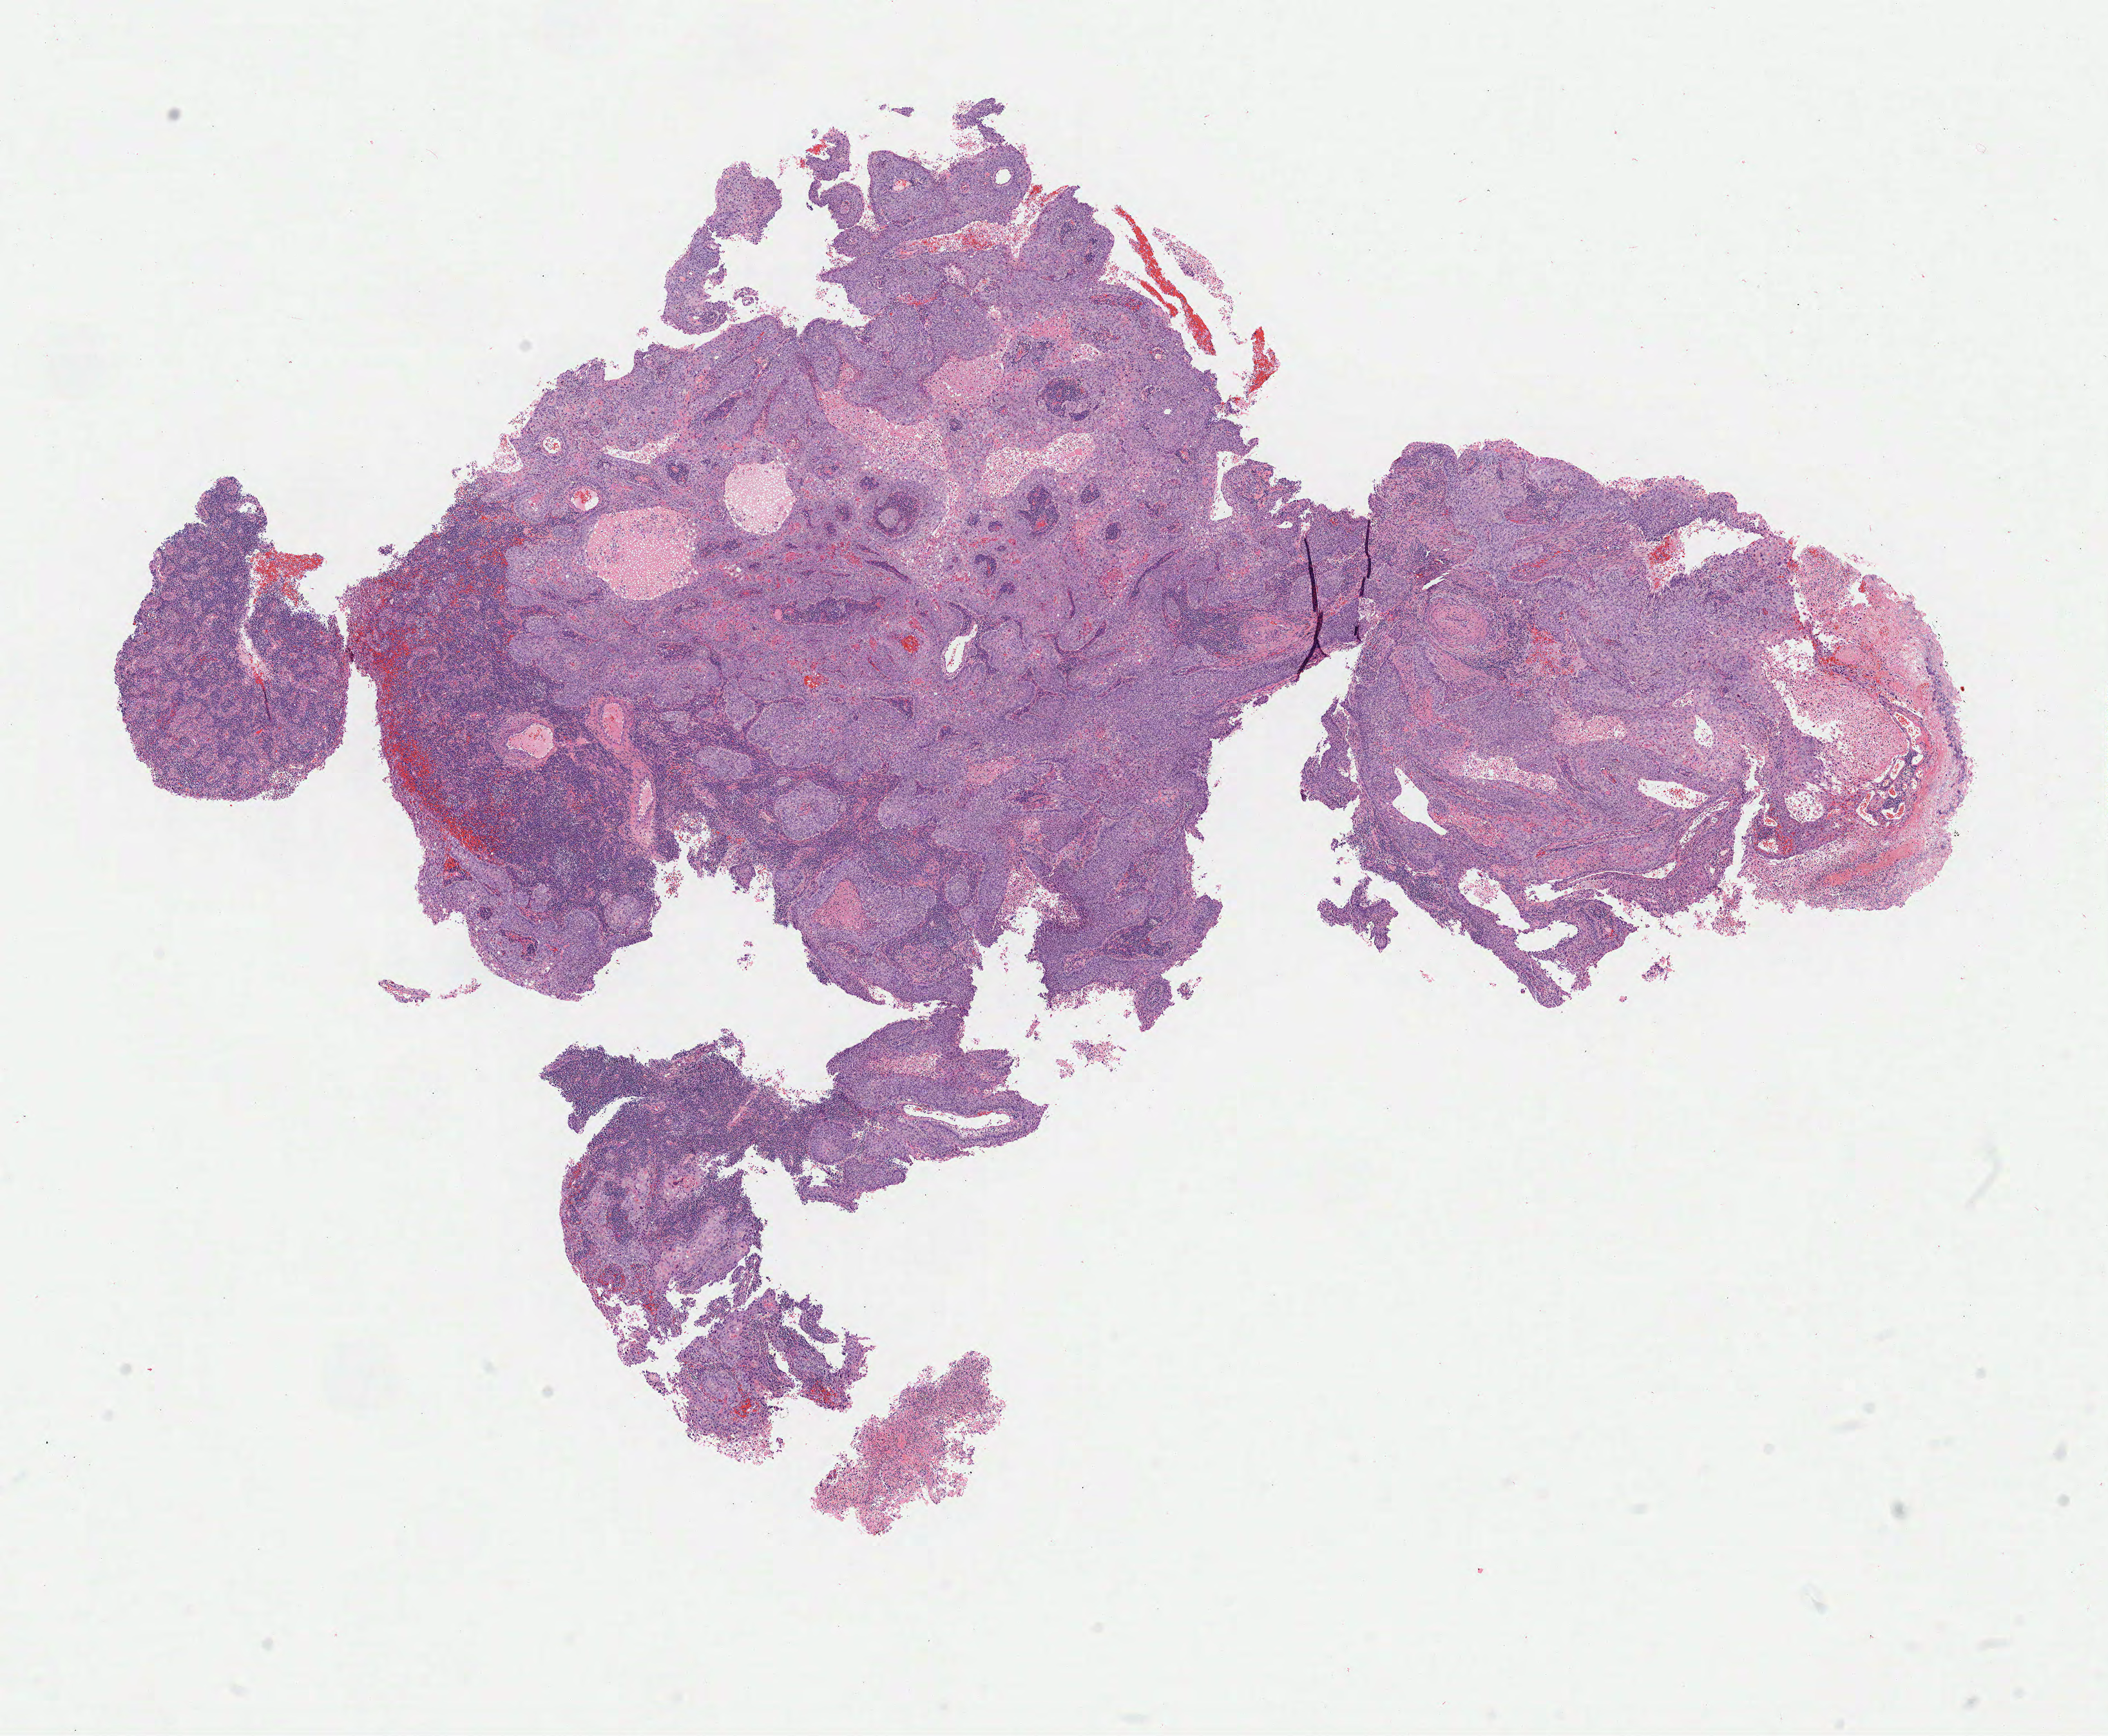
Haematoxylin and eosin whole-slide image, whole scanned area (about 13.0 x 10.7 mm) shown as a low-resolution overview, specimen: tumor tissue, anatomic site: cervix. Female patient, aged 34.
Diagnosis: Squamous cell carcinoma, large cell, nonkeratinizing, NOS.